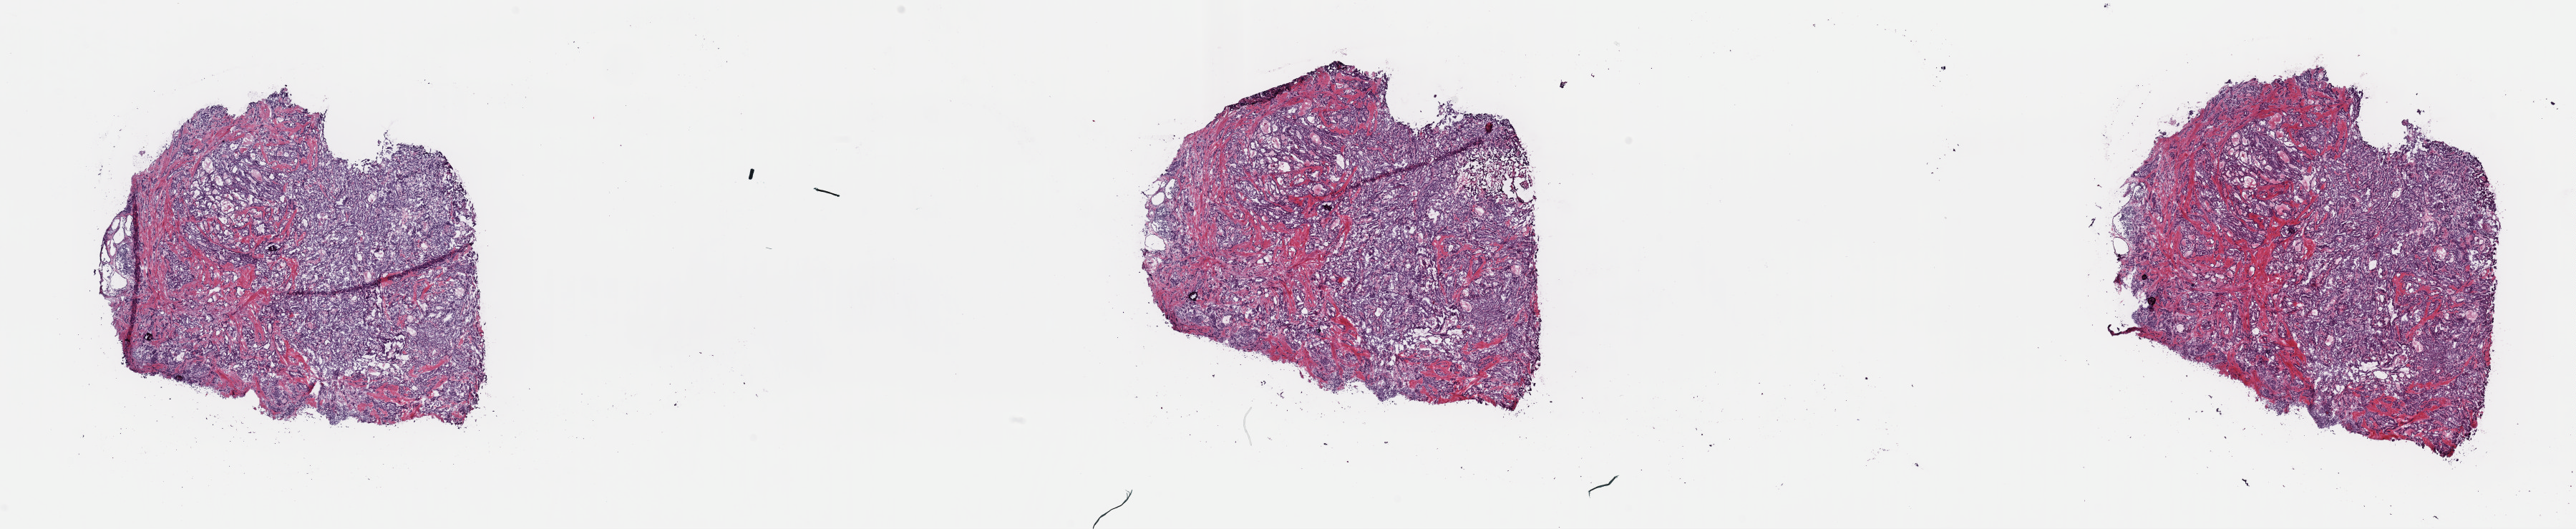
Digitized Hematoxylin and eosin (H&E) stained tissue section (whole slide), whole scanned area (about 28.4 x 5.8 mm, acquisition: 40x scan) shown as a low-resolution overview; frozen section; sample: primary tumour, thyroid. Female, age 24 years at initial diagnosis. Composition of this section per pathologist review: tumour cells 60%, tumour nuclei 100%, normal cells 0%, stromal cells 40%, necrosis 0%. Infiltration values recorded for this section: lymphocyte infiltration 2%, monocyte infiltration 0%, neutrophil infiltration 0%.
AJCC pathologic stage: I (7th edition). Diagnosis: Papillary adenocarcinoma, NOS (thyroid gland). Laterality: right. Lymph nodes positive (case pathology): 12 of 33 examined.